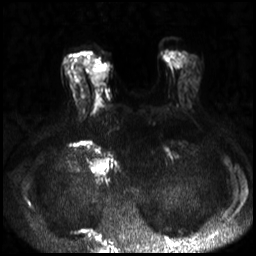
Breast MRI, one axial slice. Position 10 of 30 along the scan axis. Diffusion-weighted series; image 2 of 4 stored at this slice position (different b-values; order by instance number). 3 T. 4 mm slice thickness. 256 × 256 image matrix, field of view 320 × 320 mm. Female patient.
Structures marked on this image (expert manual segmentation):
- tumour on diffusion-weighted imaging: box from (x=92, y=64) to (x=108, y=84) px